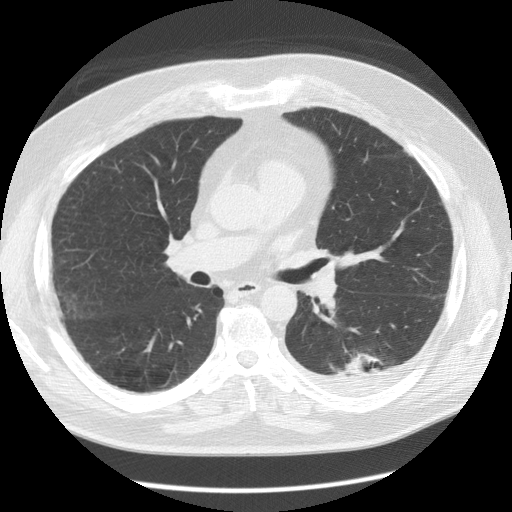
Low-dose screening chest CT, one axial slice. Slice 72 of 126 in the series (ordered by position). Reconstruction kernel STANDARD. Lung window (W 1500 / L -600 HU). 2.5 mm slice thickness. 512 × 512 image matrix.
Annotated regions visible in this slice (expert manual segmentation):
- lesion 1 (tumor, lower lobe of left lung): bounding box [x1, y1, x2, y2] px = [341, 353, 382, 375]